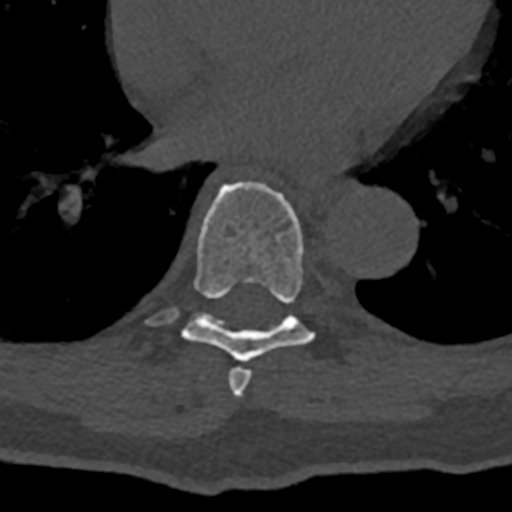
CT including the spine, one axial slice. Position 708 of 797 along the scan axis. Bone window (W 1800 / L 400 HU). 0.5 mm slice thickness. 512 × 512 image matrix. Male patient, age 74 years. From the clinical record (not read from this slice): primary cancer: renal; vertebrae with lytic lesions (as recorded): T10, L1, L2, L3, L4, L5.
Structures marked on this image (semi-automatic segmentation, software-assisted and operator-edited):
- T7 vertebra: bounding box <228,368,252,399> (left, top, right, bottom; pixels)
- T8 vertebra: <144,182,319,362>